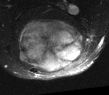
MRI of an extremity soft-tissue mass, one axial slice; slice 29 of 52 in the series (ordered by position); T2-weighted fat-saturated; MR volume resampled by the dataset authors to the PET/CT grid (not the native acquisition matrix); 109 × 95 image matrix, field of view 106 × 93 mm. Male patient. From the clinical record (not read from this slice): histological type: synovial sarcoma; site of the primary tumour: left poplietal fossa.
Annotated regions visible in this slice (expert contour drawn on MRI and transferred to this co-registered scan by the dataset authors):
- gross tumour volume (mass): bounding box <17,19,86,71> (left, top, right, bottom; pixels)